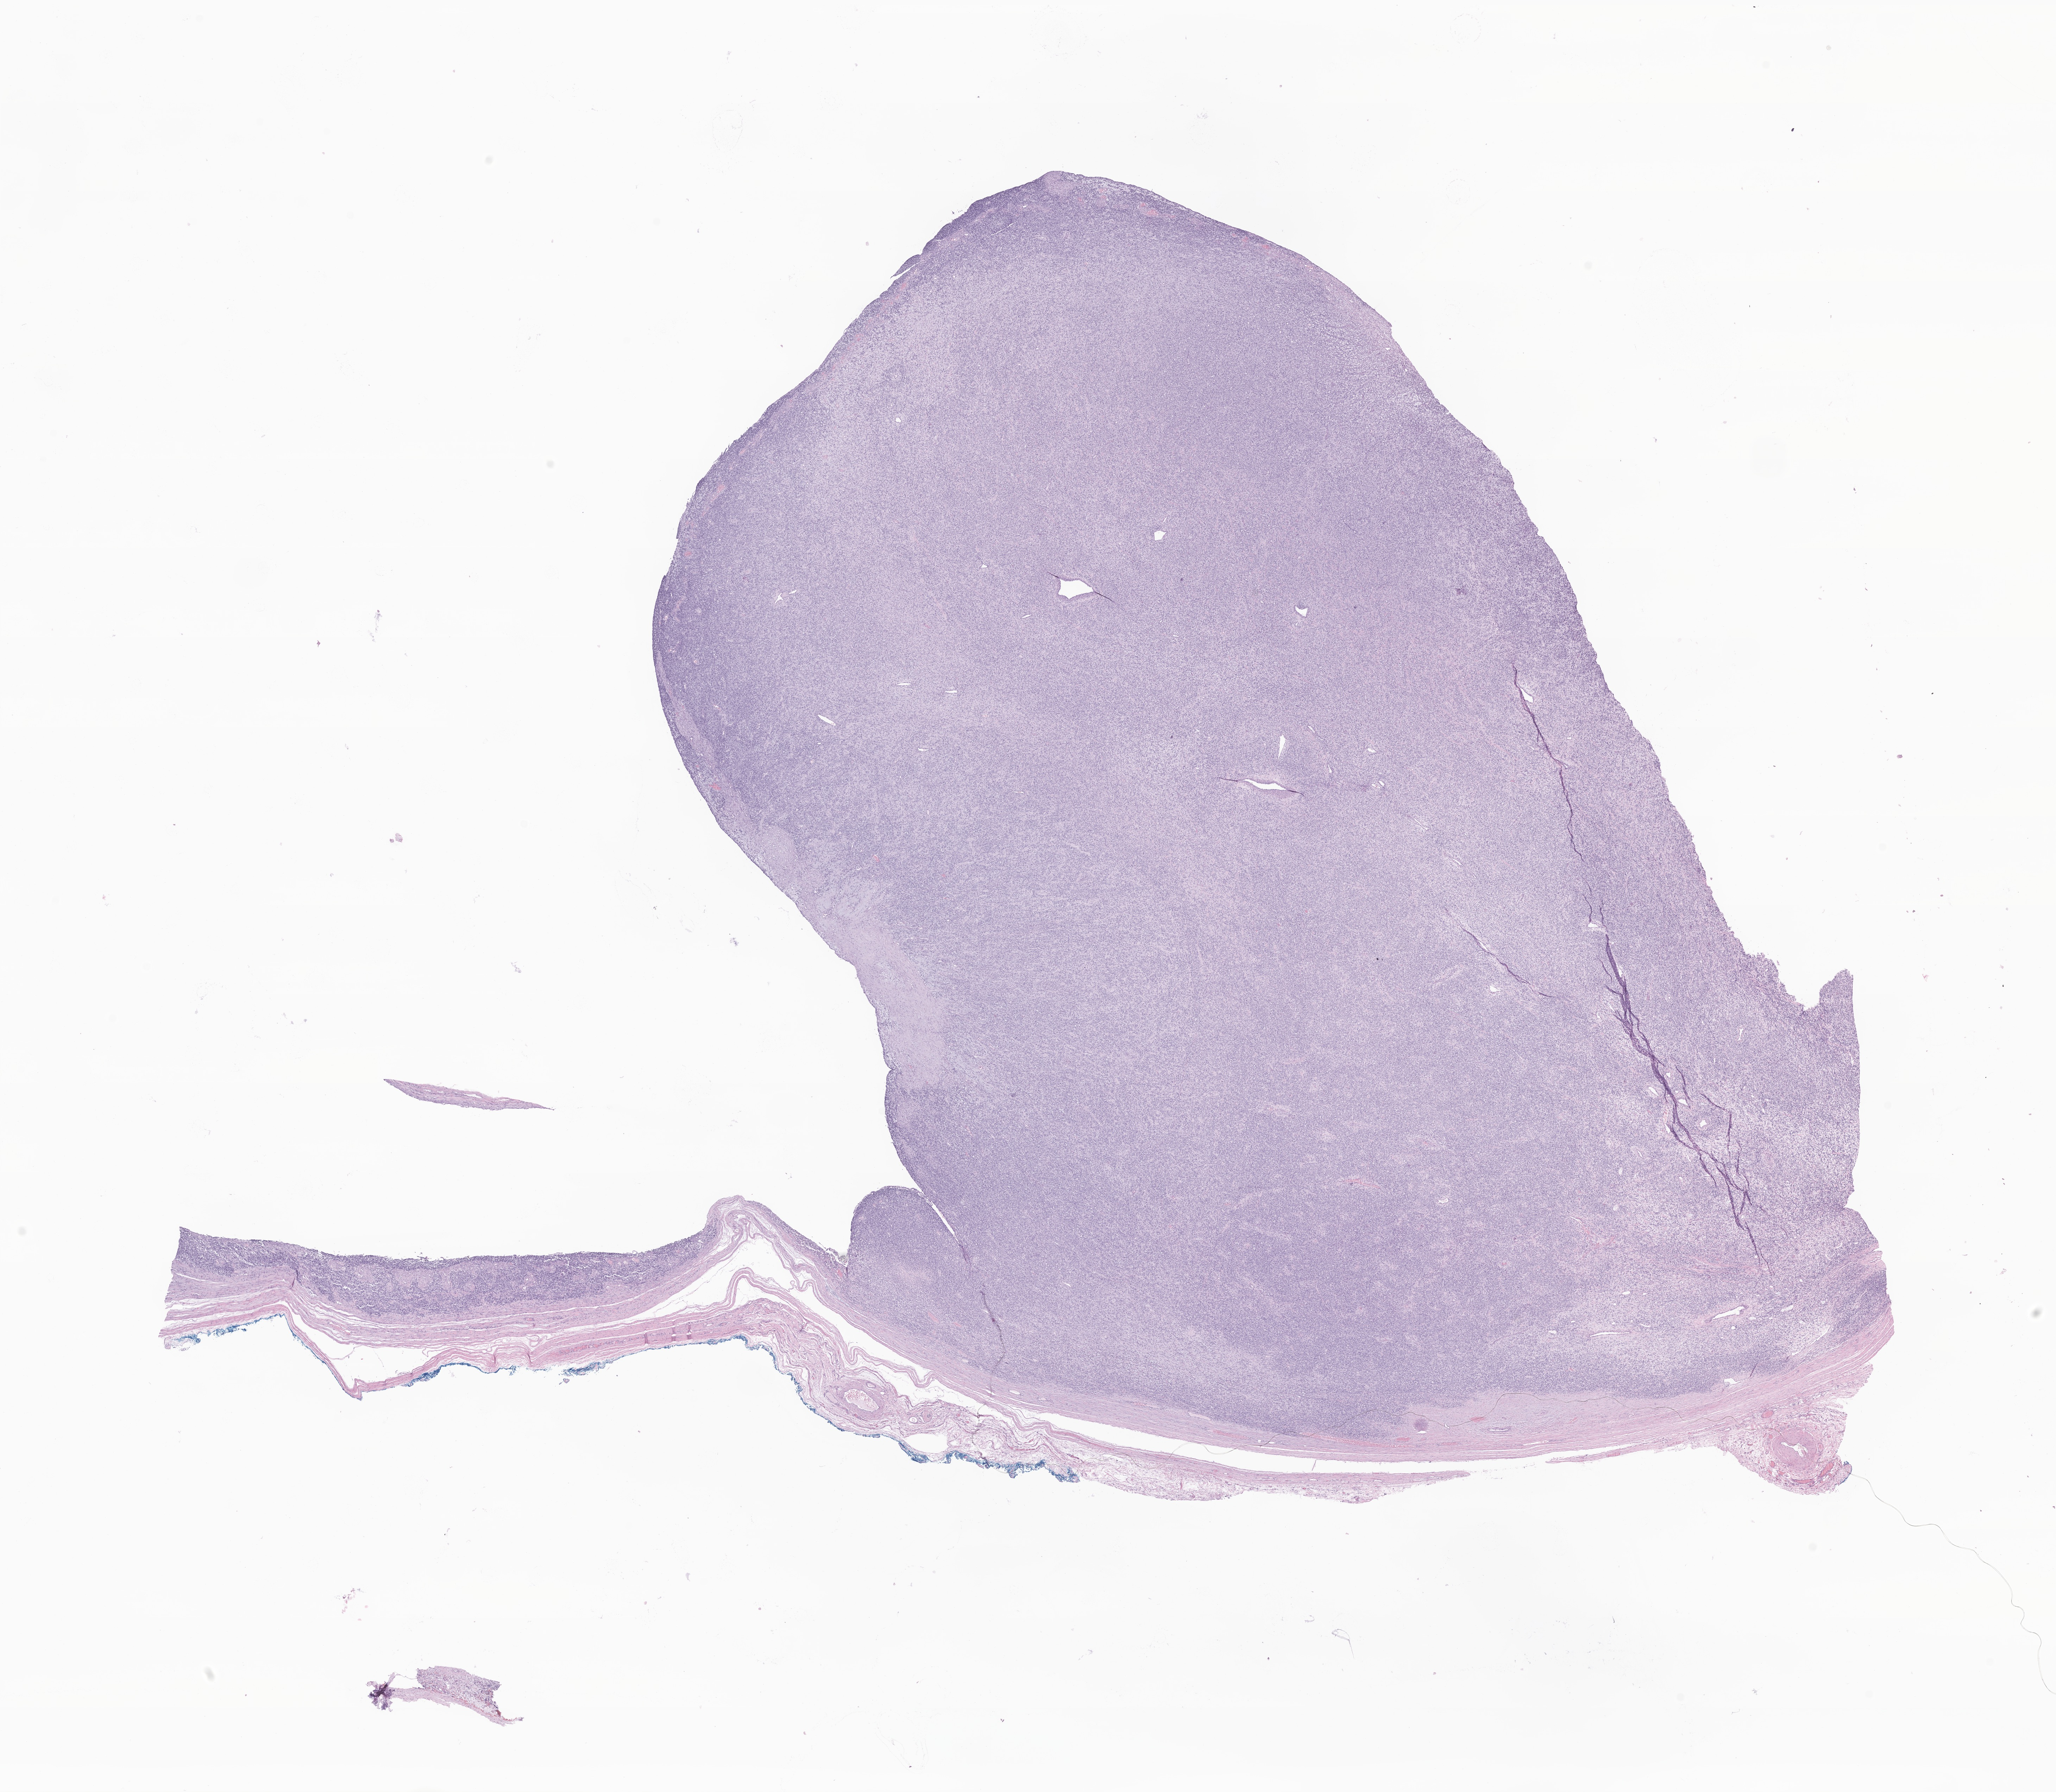
Digitized H&E-stained section of tumor tissue from the testis — shown as a low-resolution overview of the whole scanned area (about 24.6 x 21.5 mm), formalin-fixed, paraffin-embedded (FFPE) tissue. Male patient, age 172 months (14 years 4 months).
* recorded diagnosis: Alveolar rhabdomyosarcoma